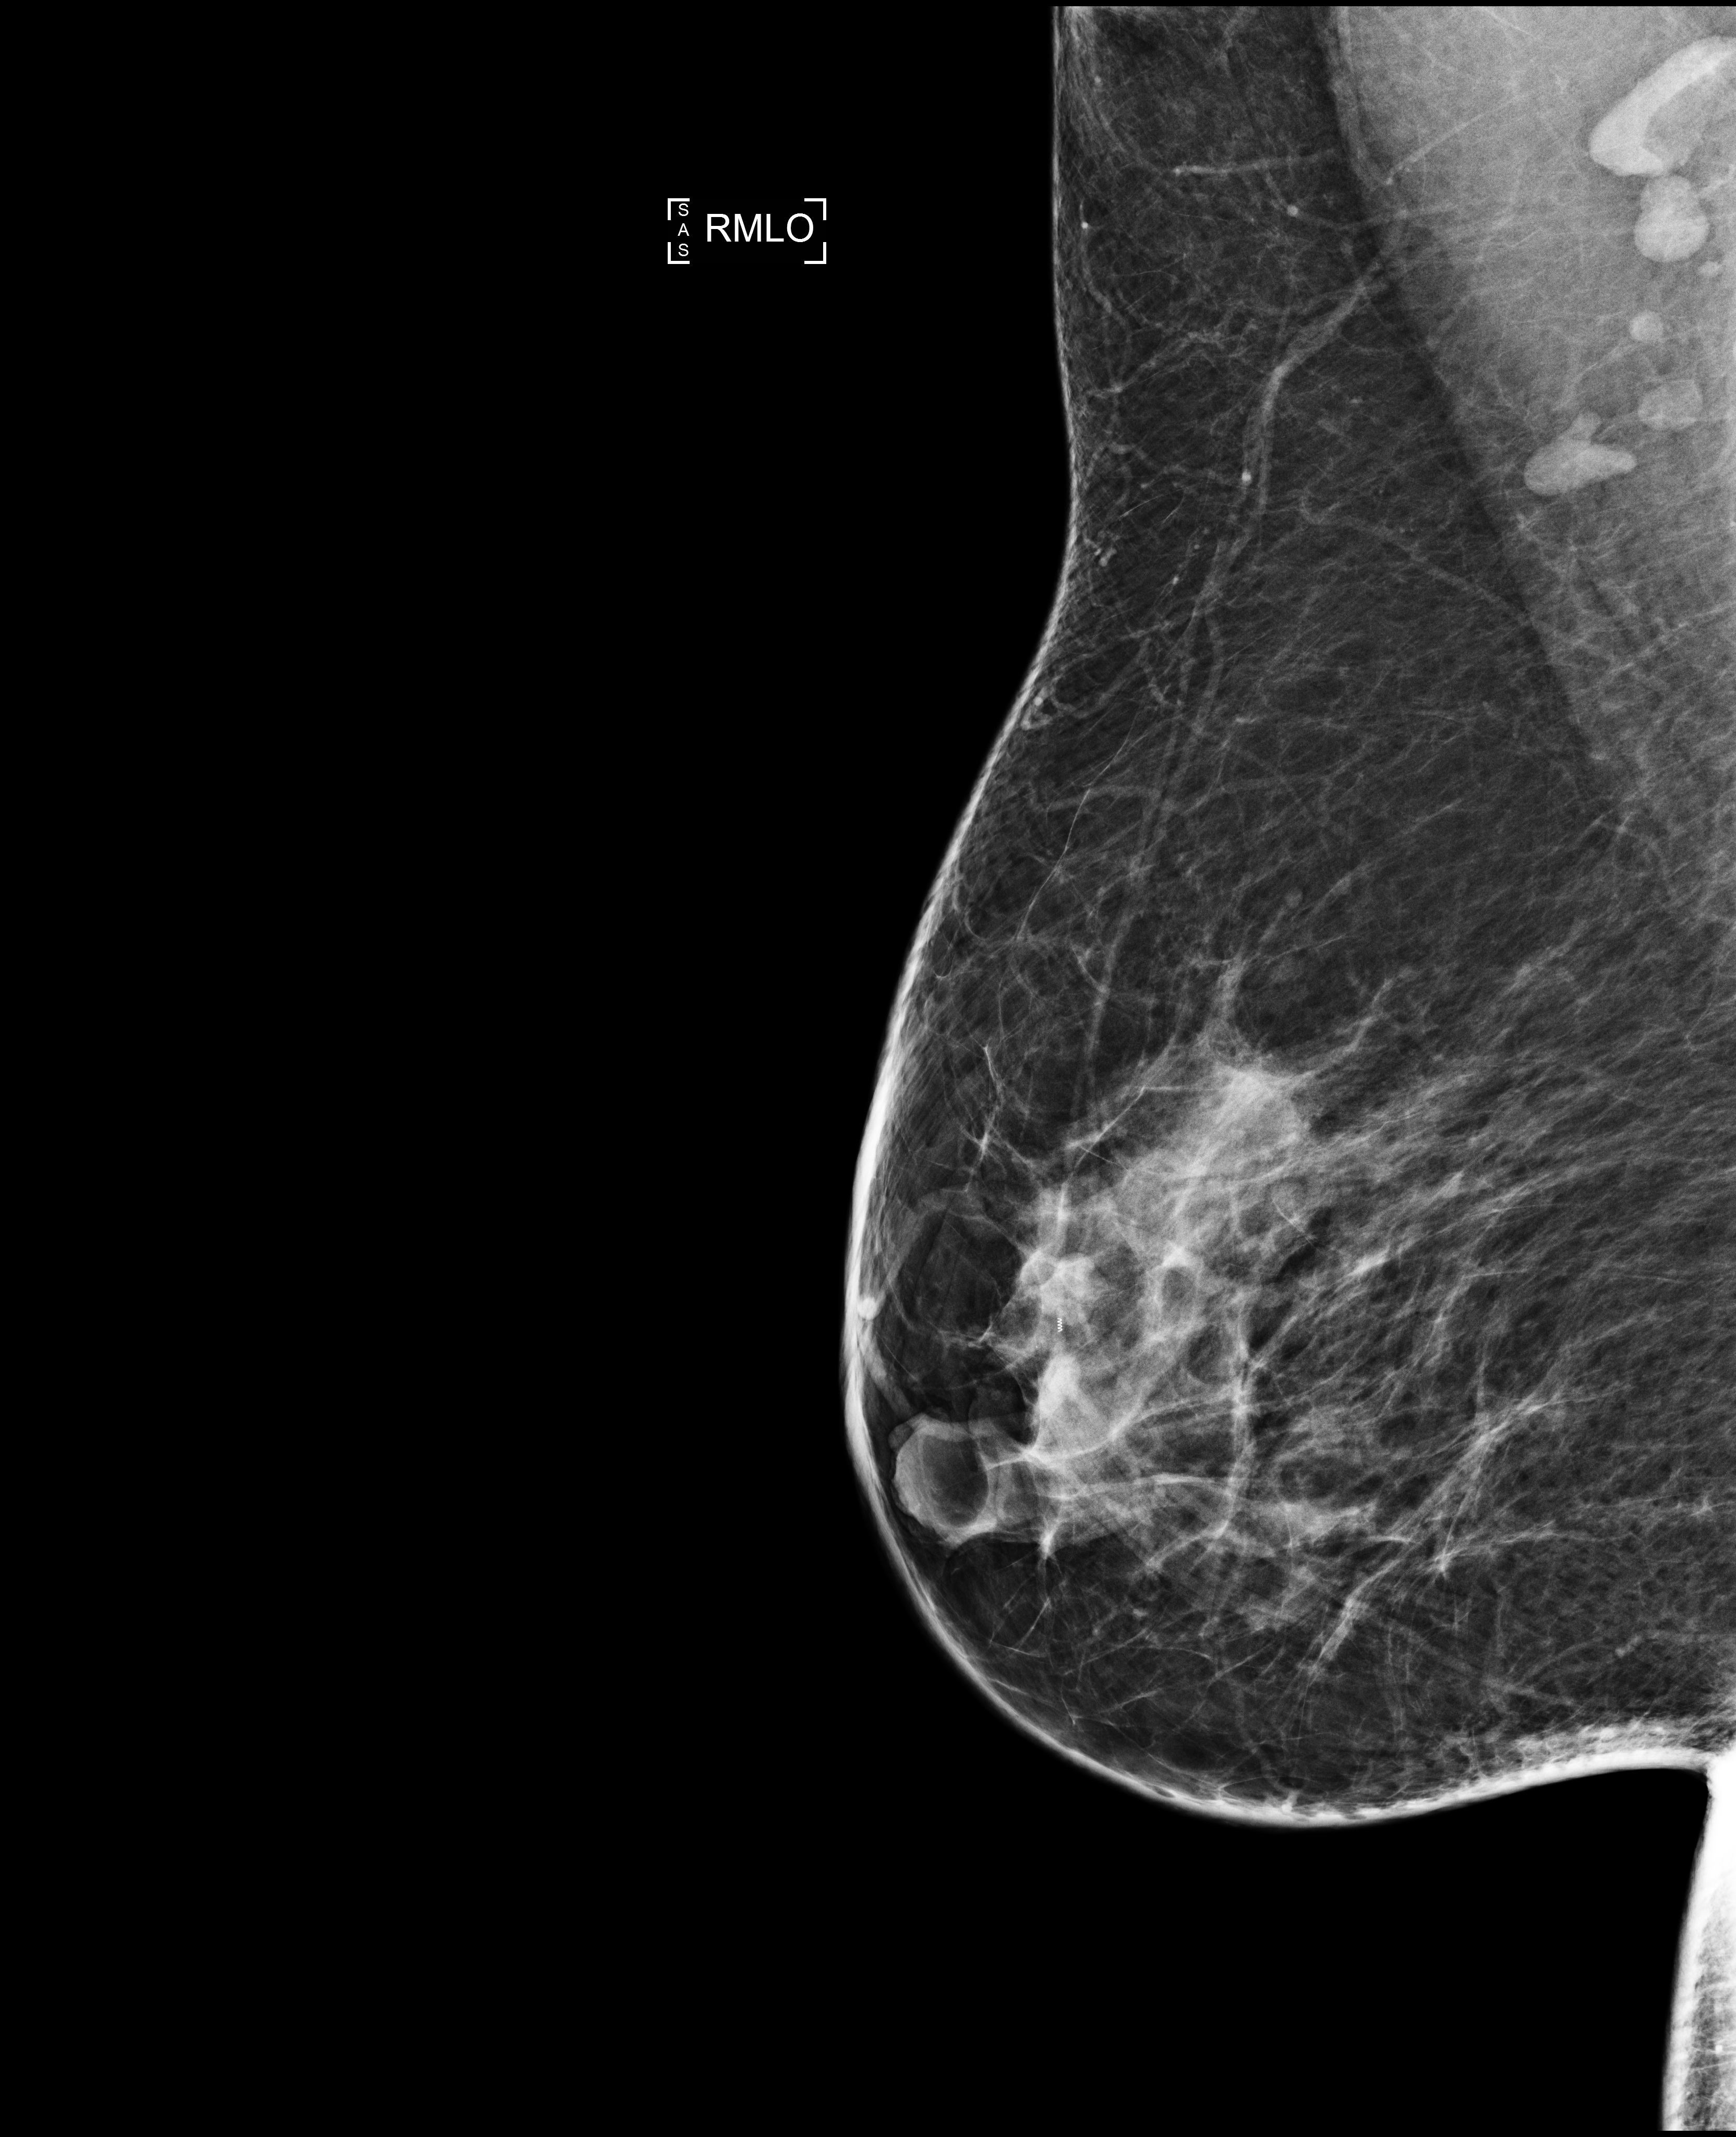
Digital mammogram (FFDM), right breast, mediolateral oblique (MLO) view, annual screening mammography examination, compressed breast thickness 69 mm. Patient aged 46 years (female).
Breast density at the screening exam (both breasts): heterogeneously dense (BI-RADS density category c). Final BI-RADS category for the screening round (tomosynthesis exam, both breasts): category 1. Recall: no recall after this screen.